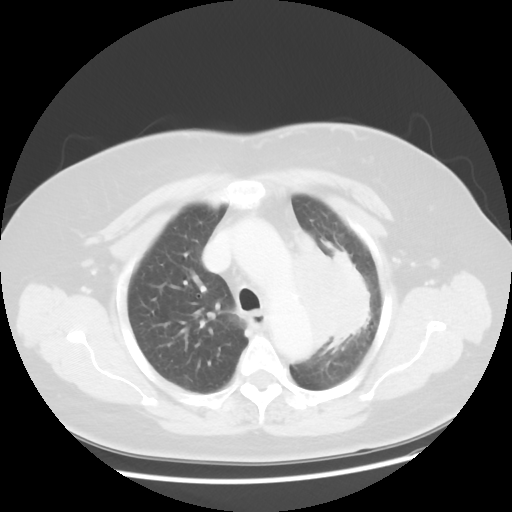
Chest CT, one axial slice. Slice 35 of 49 in the series (ordered by position). Reconstruction kernel STANDARD. 120 kVp. Lung window (W 1500 / L -600 HU). 5 mm slice thickness. 512 × 512 image matrix, field of view 374 × 374 mm. Patient: female, 58 years. Case-level facts recorded for this patient, not image findings: clinical TNM (as recorded): T4 N3 M0; histopathological grade: G3.
Annotated regions visible in this slice (rectangle marked by the reading radiologist):
- lung tumour (recorded histology: small cell carcinoma): bounding box [x1, y1, x2, y2] px = [287, 218, 380, 355]